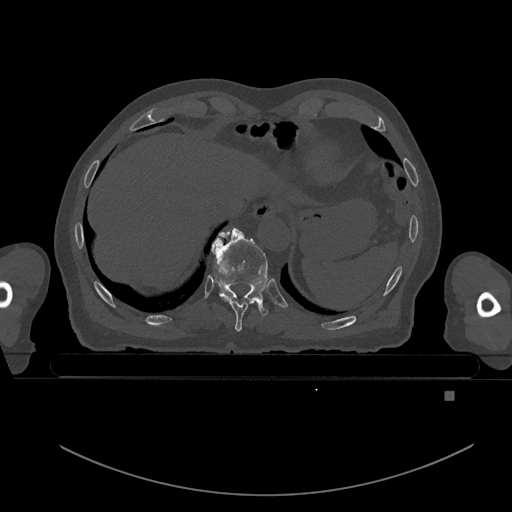
CT including the spine, one axial slice. Slice 114 of 969 in the series (ordered by position). Bone window (W 1800 / L 400 HU). 0.5 mm slice thickness. 512 × 512 image matrix, field of view 456 × 456 mm. Patient: male, 82 years. Case-level facts recorded for this patient, not image findings: primary cancer: prostate; vertebrae with lytic lesions (as recorded): T11, T9, T8, T2.
Annotated regions visible in this slice (semi-automatically segmented with operator editing):
- T10 vertebra: box from (x=211, y=227) to (x=268, y=316) px
- T9 vertebra: (x=219, y=232)–(x=258, y=332)